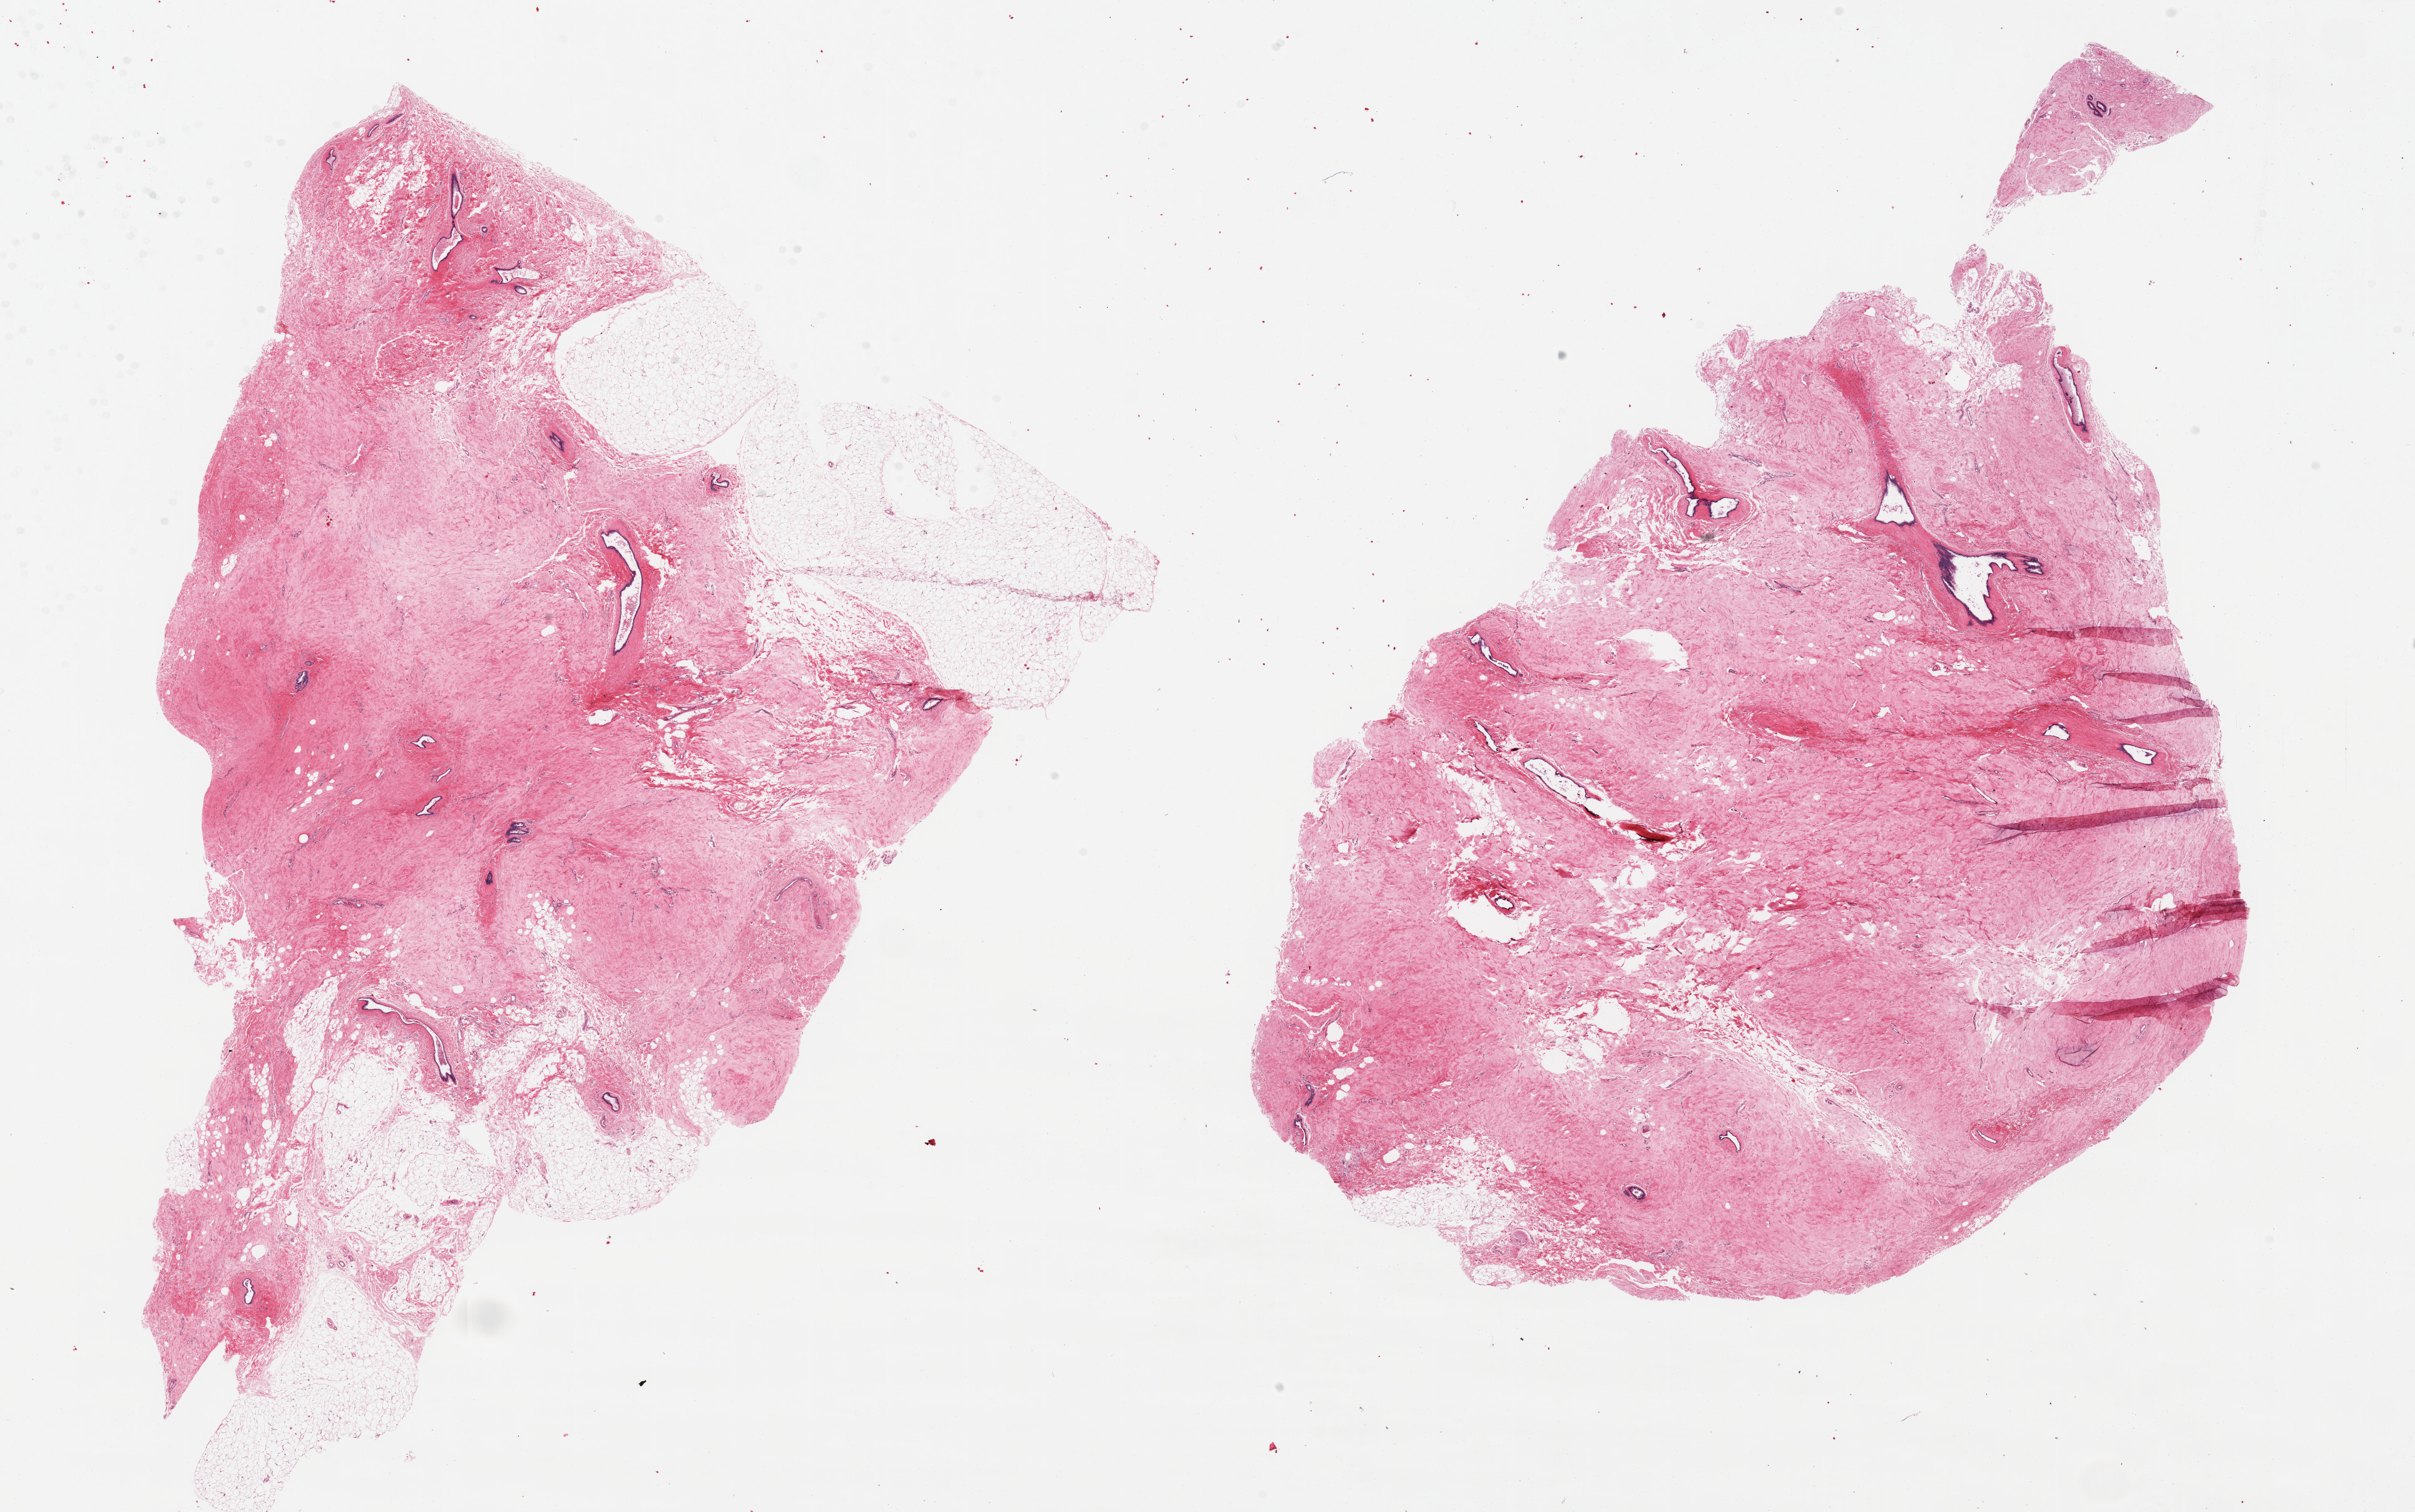
Digitized haematoxylin and eosin-stained section, brightfield — shown as a low-resolution overview of the whole scanned area (about 30.5 x 19.1 mm); PAXgene-fixed, paraffin-embedded tissue; target tissue: breast; donor tissue sample.
Reviewer comment on this tissue sample: 2 pieces ~14x11mm; Stromal fibrosis, rare ductal elements seen.